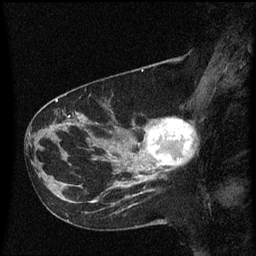
Breast MRI (dynamic contrast-enhanced), one sagittal slice. Position 25 of 60 along the scan axis. Dynamic contrast-enhanced series, image 2 of 3 at this slice position (ordered by acquisition). 1.5 T. TE 4.2 ms, TR 8.4 ms. 2 mm slice thickness. 256 × 256 image matrix. Female patient, age 41 years. Case-level facts recorded for this patient, not image findings: setting: breast cancer imaged before/during neoadjuvant chemotherapy; receptor status: triple-negative.
Outlined on this slice (semi-automatically segmented with operator editing):
- analysis volume of interest (the breast-tissue region the enhancement analysis was run in; not a lesion): box from (x=138, y=118) to (x=195, y=177) px
- tumour enhancement mask (voxels above the 70 % enhancement threshold inside the analysis volume of interest): (x=148, y=118)–(x=194, y=167)